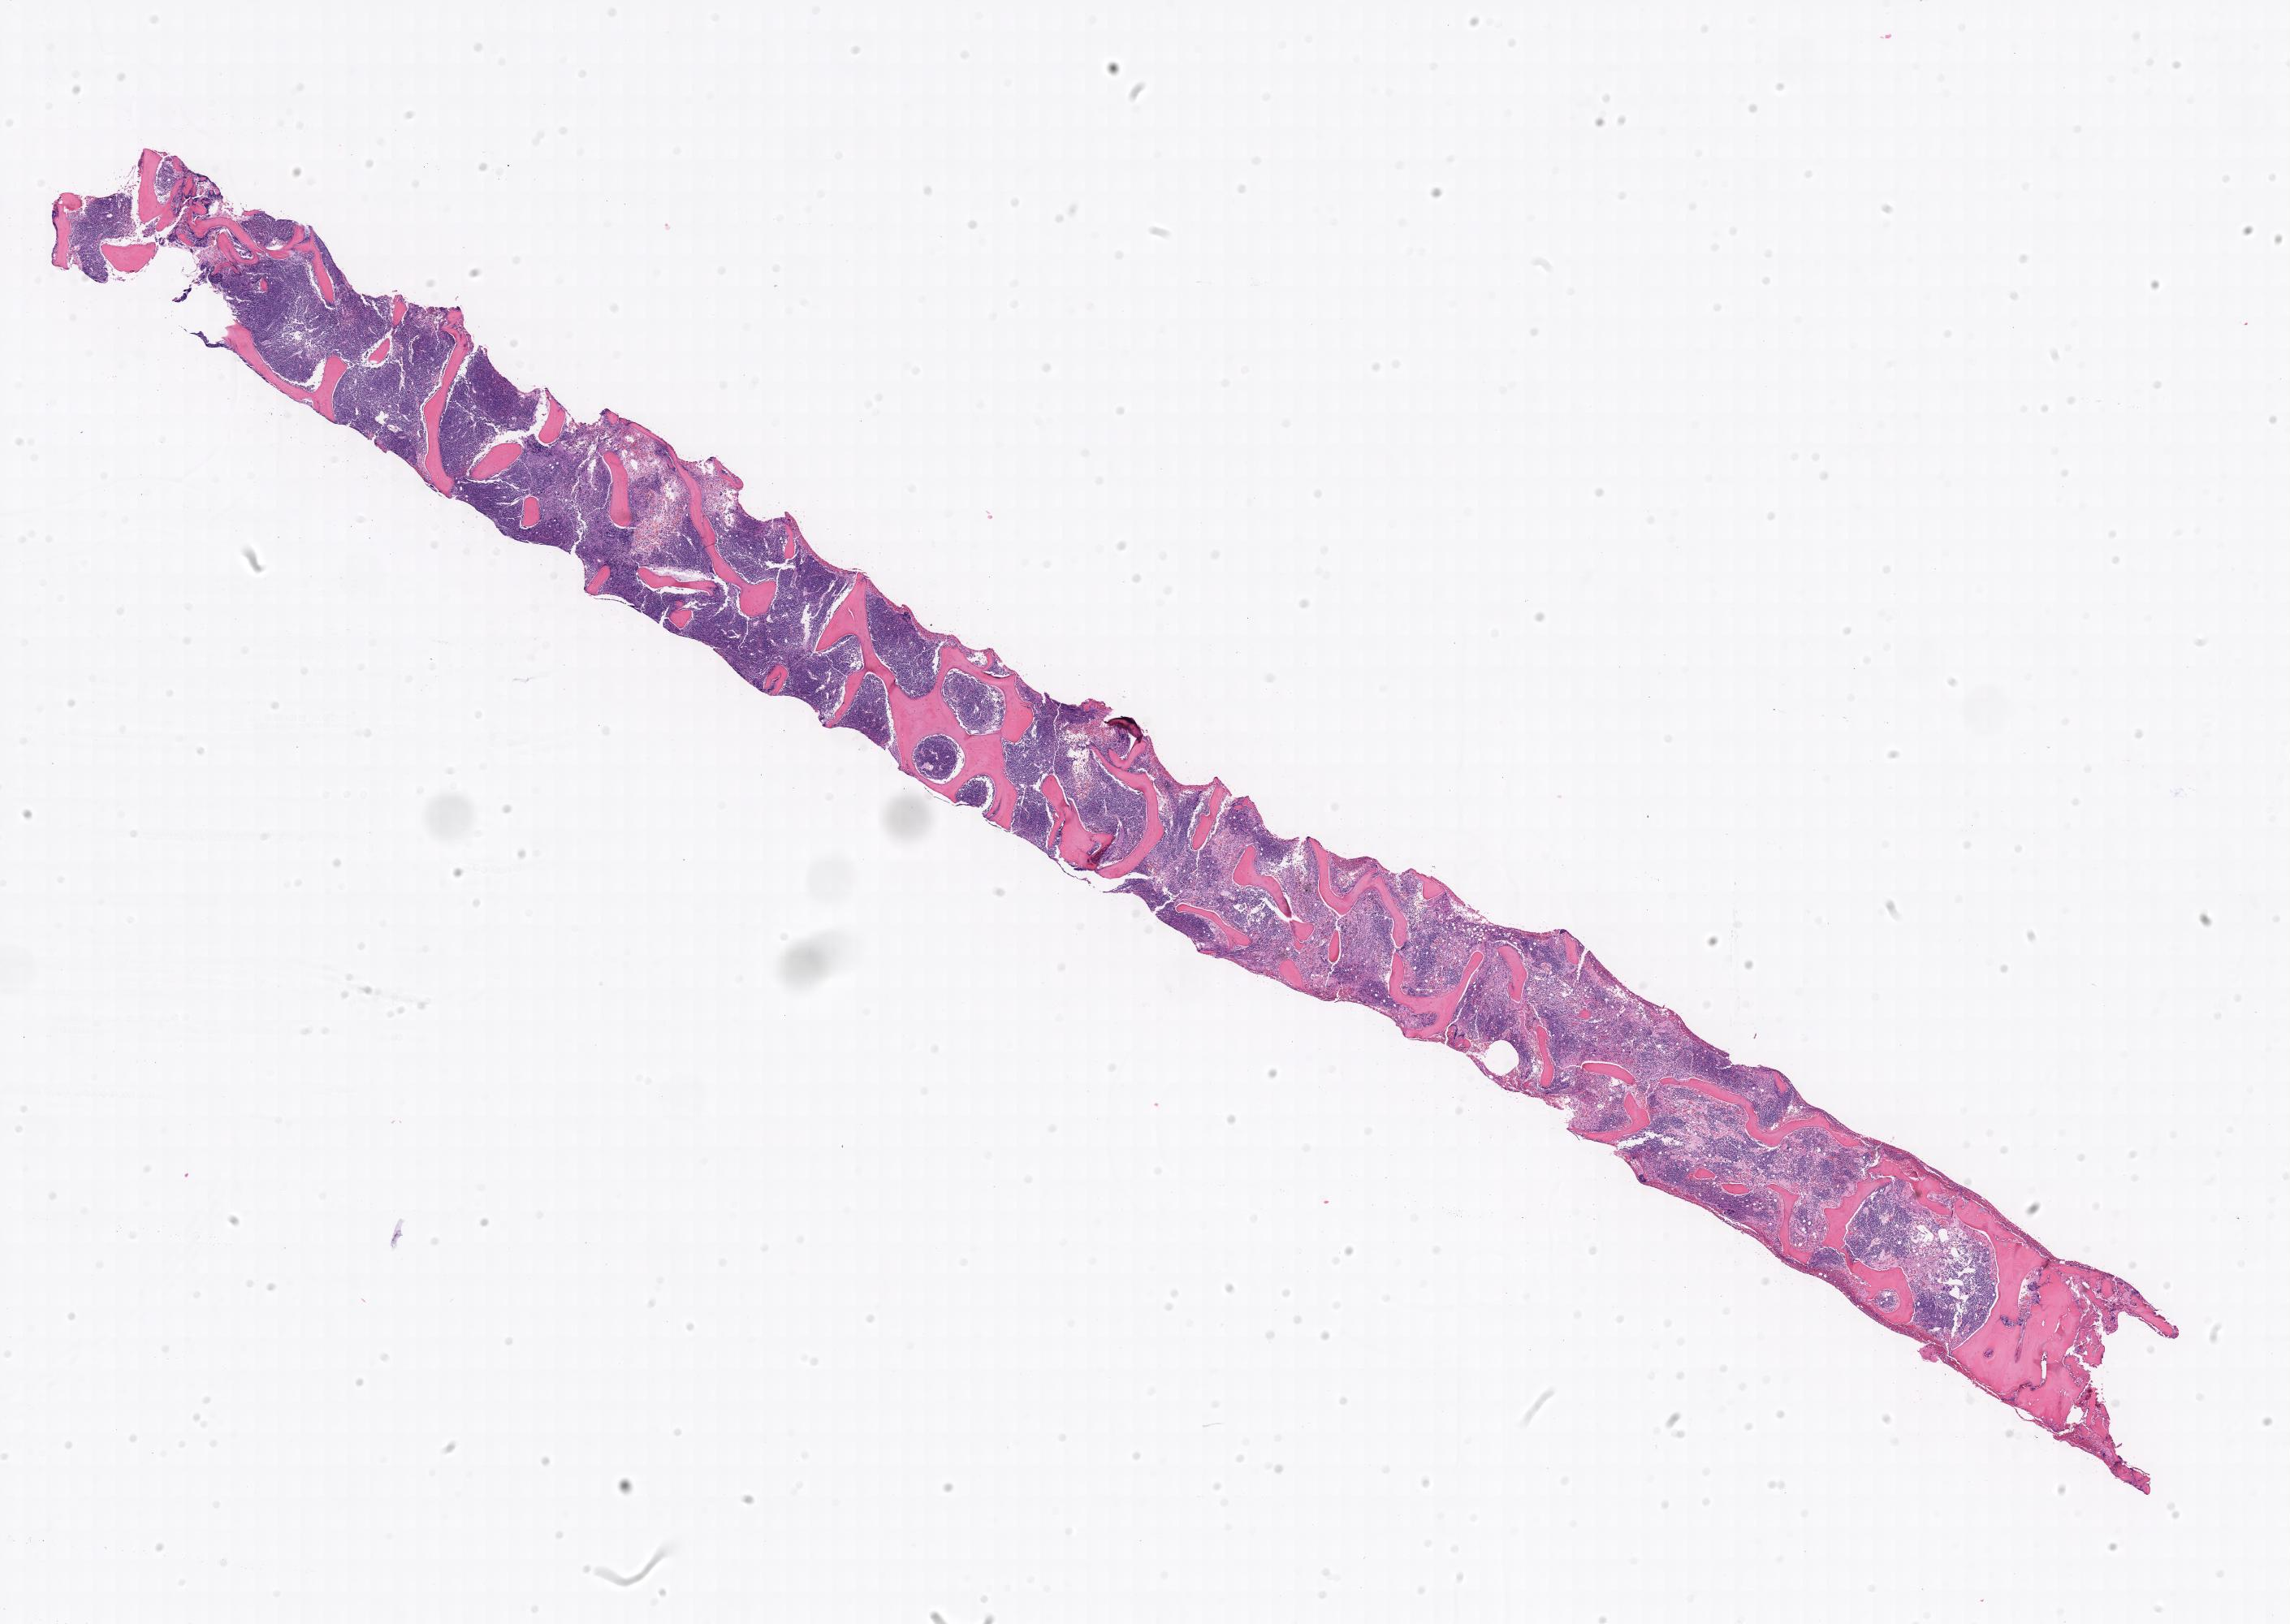
Whole-slide image, H&E stain, a low-resolution overview of the entire scanned area. Tumor tissue. Site: bone marrow. Patient: male, aged 18.
Histologic diagnosis: Burkitt lymphoma, NOS.